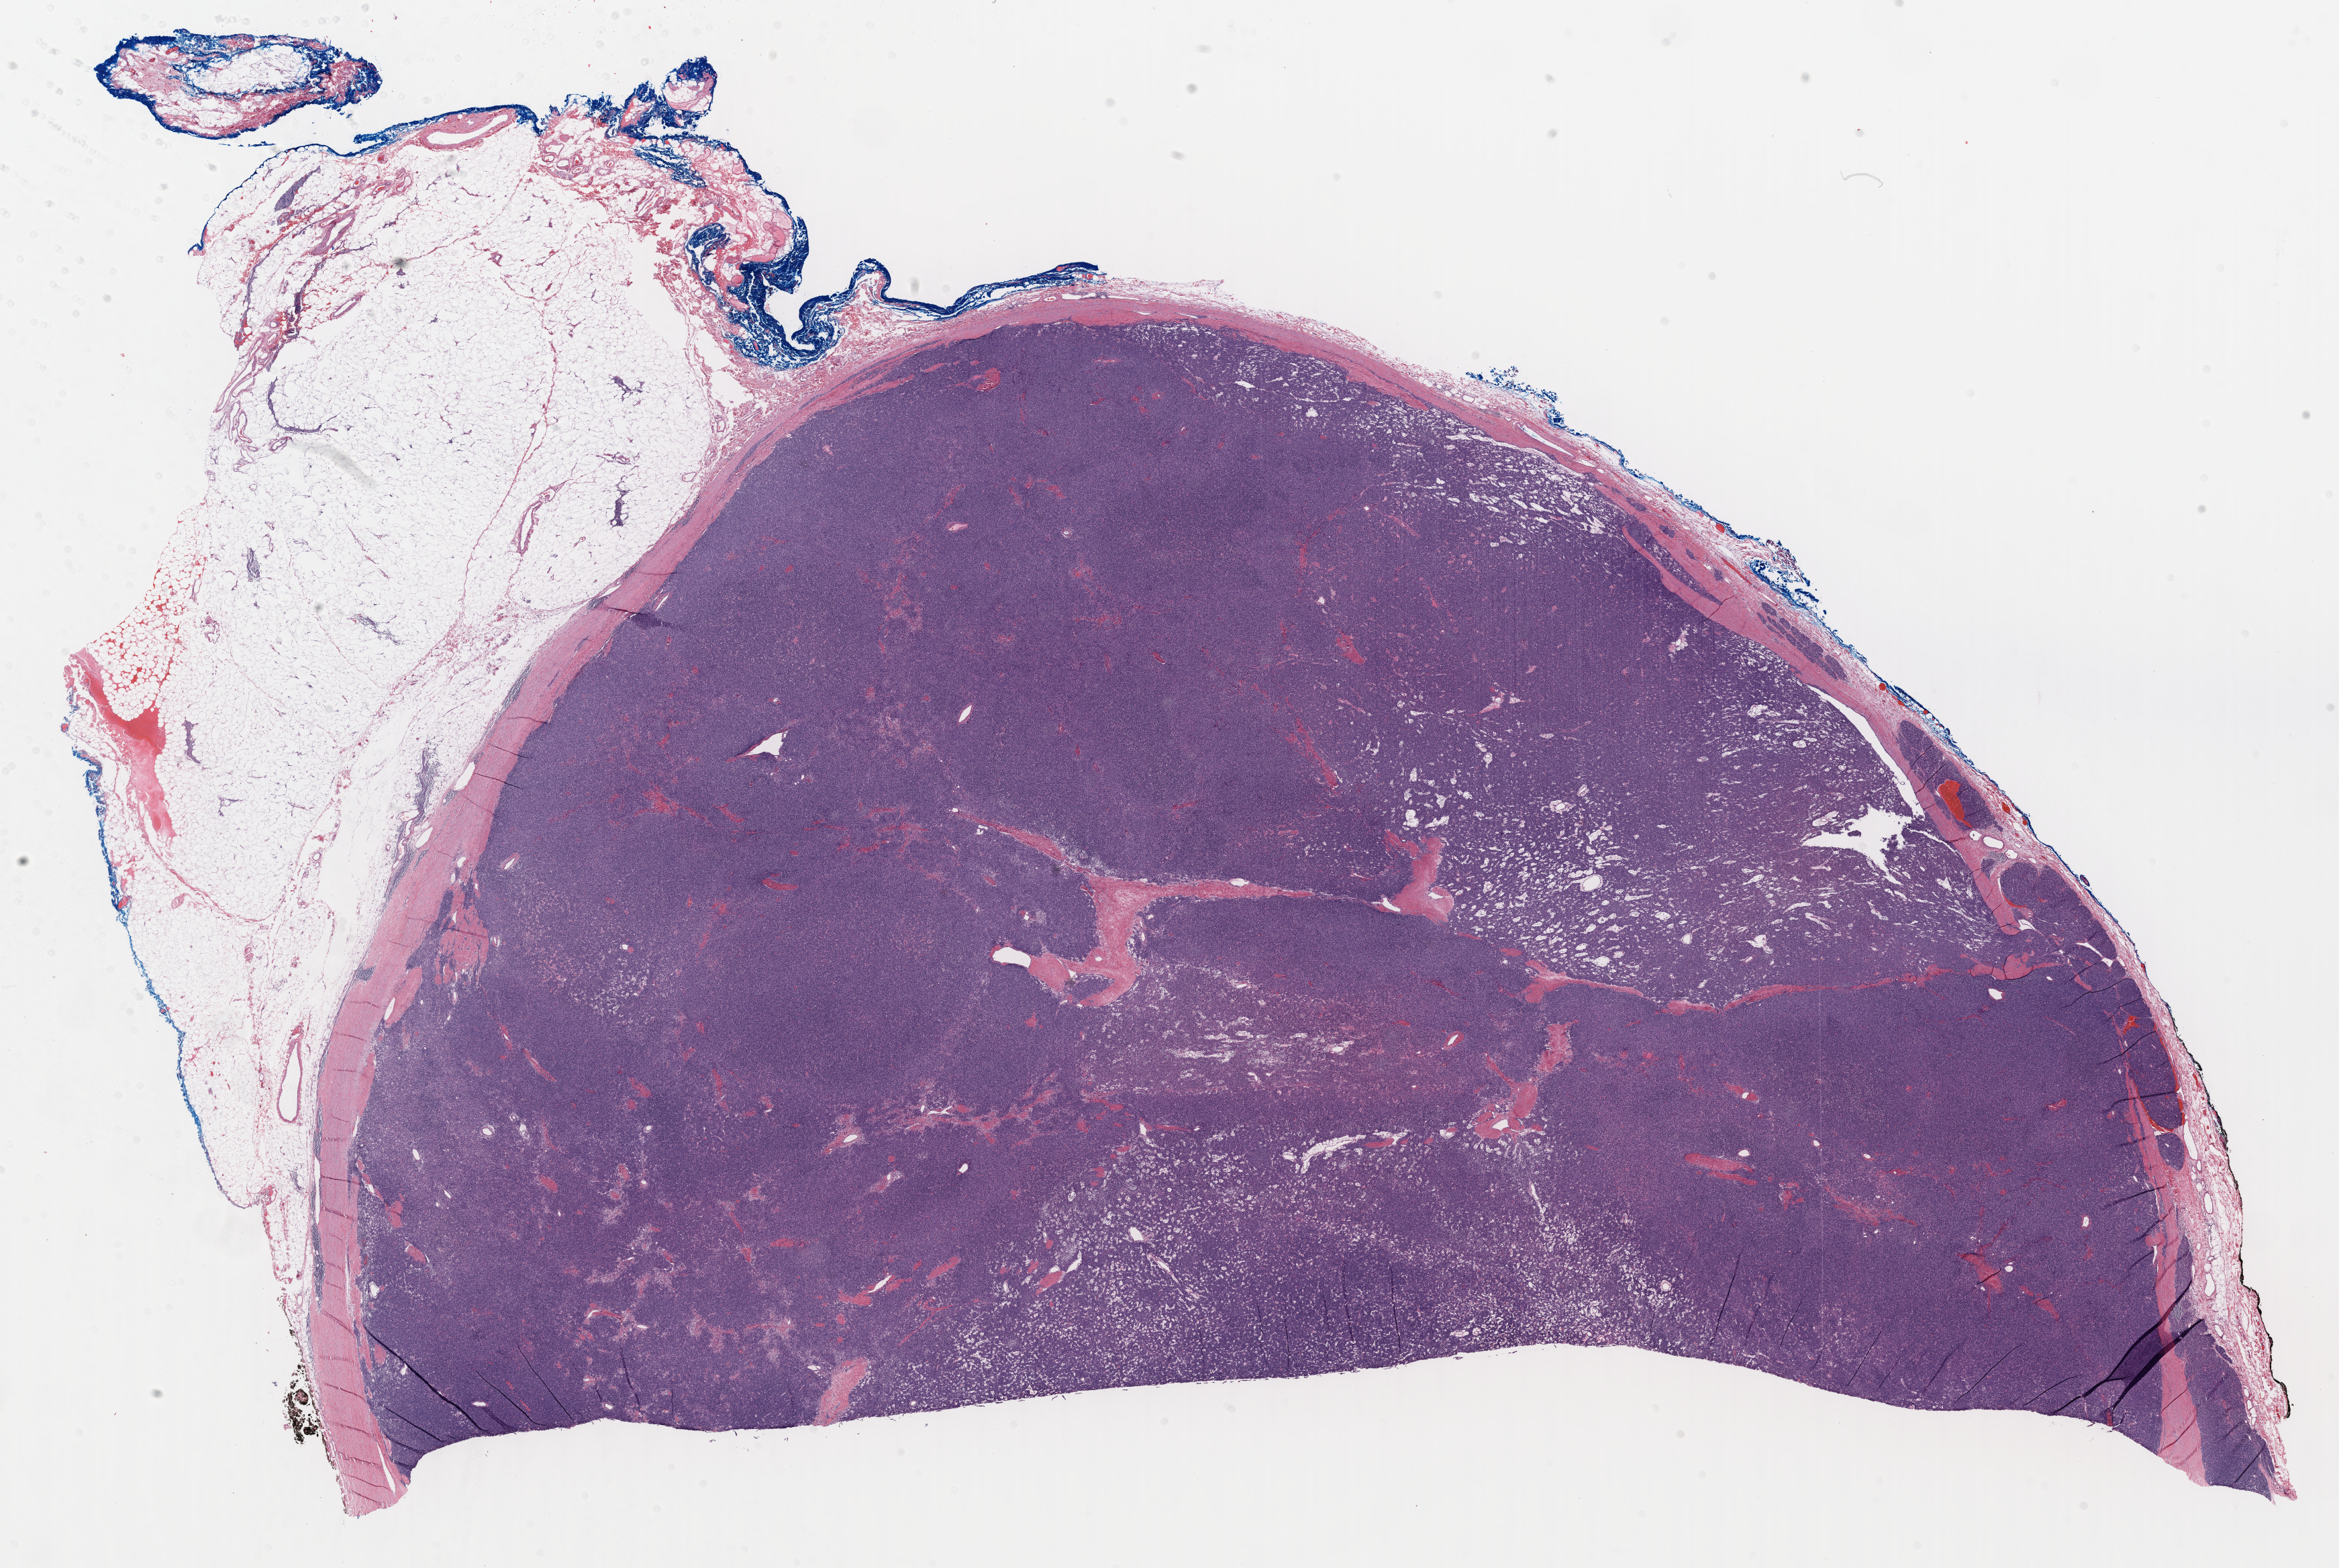
Hematoxylin and eosin (H&E) stained whole-slide image, a low-resolution overview of the entire scanned area, about 28.2 x 18.9 mm; formalin-fixed paraffin-embedded (FFPE) diagnostic section; primary tumour sample from the thymus. Male, age 67 years at initial diagnosis.
Pathologic diagnosis: Thymoma, type AB, NOS.